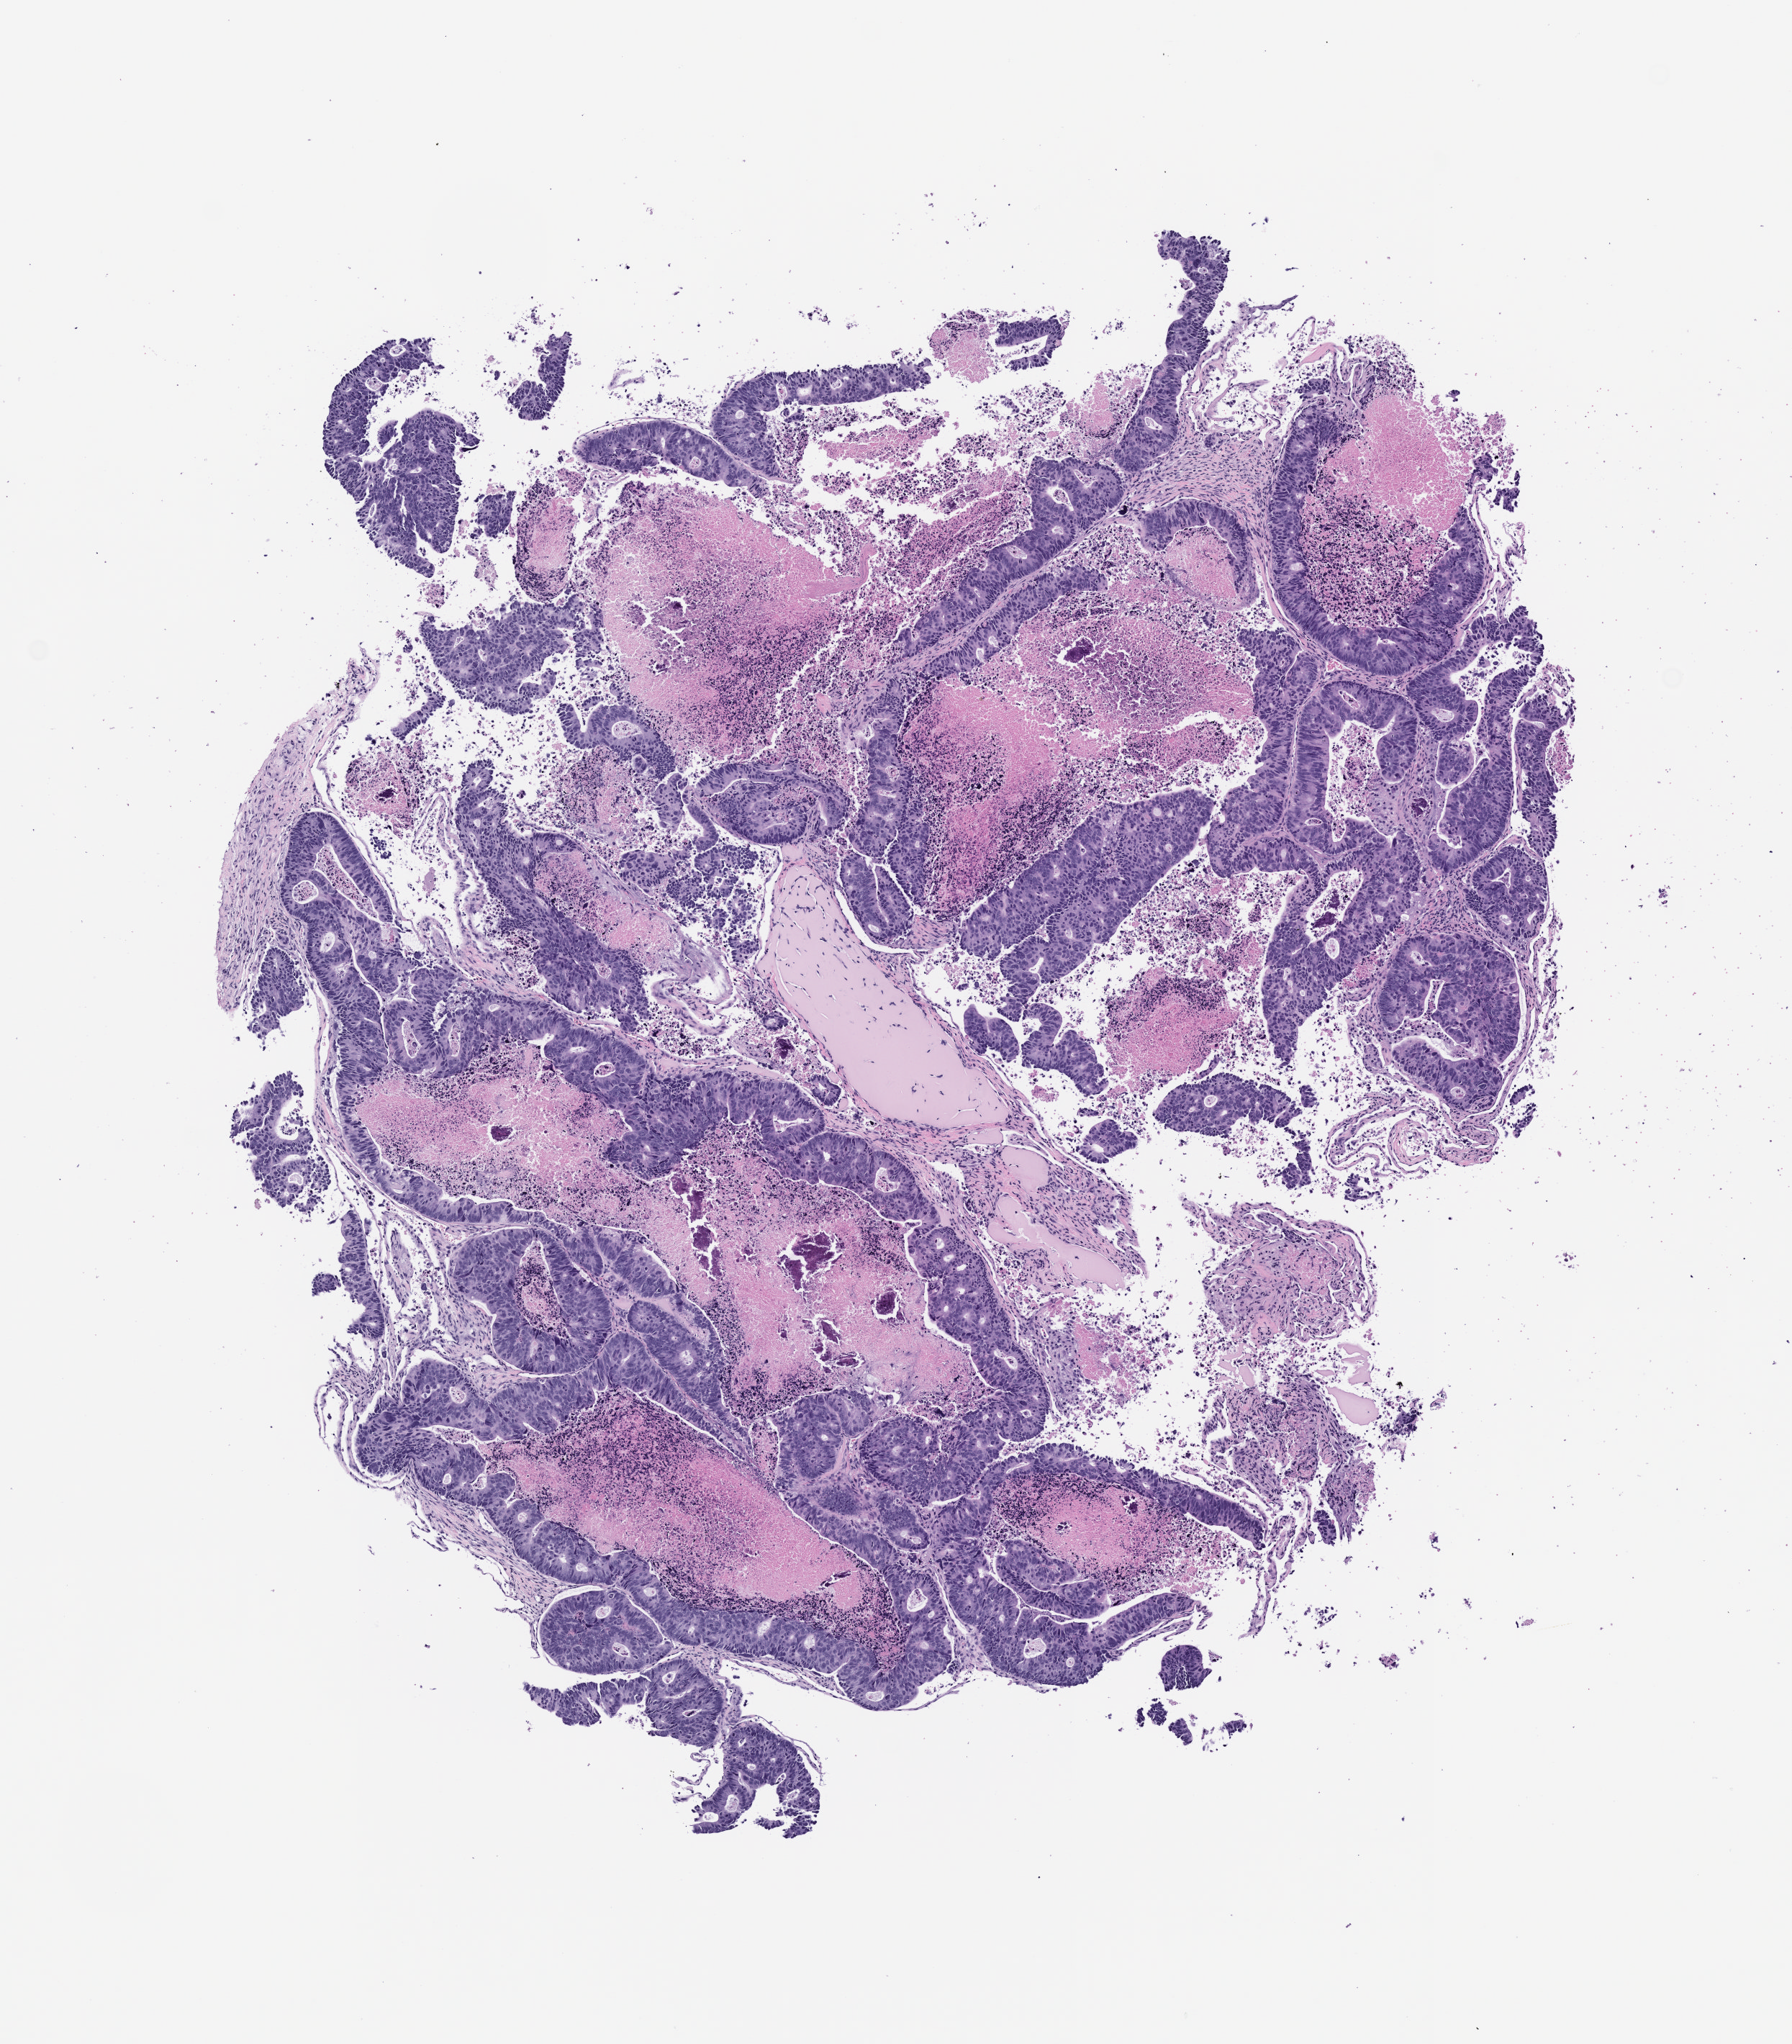
Whole-slide image, haematoxylin and eosin: patient-derived xenograft (human tumor grown in a mouse), passage 2 — a low-resolution overview of the entire scanned area, about 5.0 x 5.7 mm; FFPE section; tumor site category: colon.
Originating patient diagnosis: Colon Adenocarcinoma.